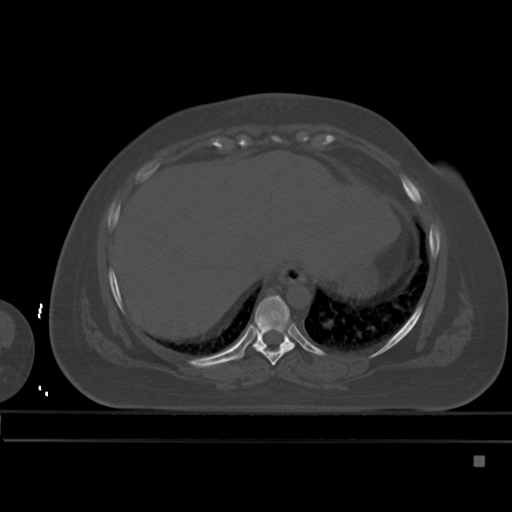
CT including the spine, one axial slice; bone window (W 1800 / L 400 HU); 512 × 512 image matrix, field of view 404 × 404 mm. Patient: female, 33 years. Case-level facts recorded for this patient, not image findings: primary cancer: breast; vertebrae with lytic lesions (as recorded): T1.
Structures marked on this image (semi-automatically segmented with operator editing):
- T8 vertebra: bounding box [x1, y1, x2, y2] px = [254, 346, 295, 366]
- T9 vertebra: [252, 295, 296, 351]